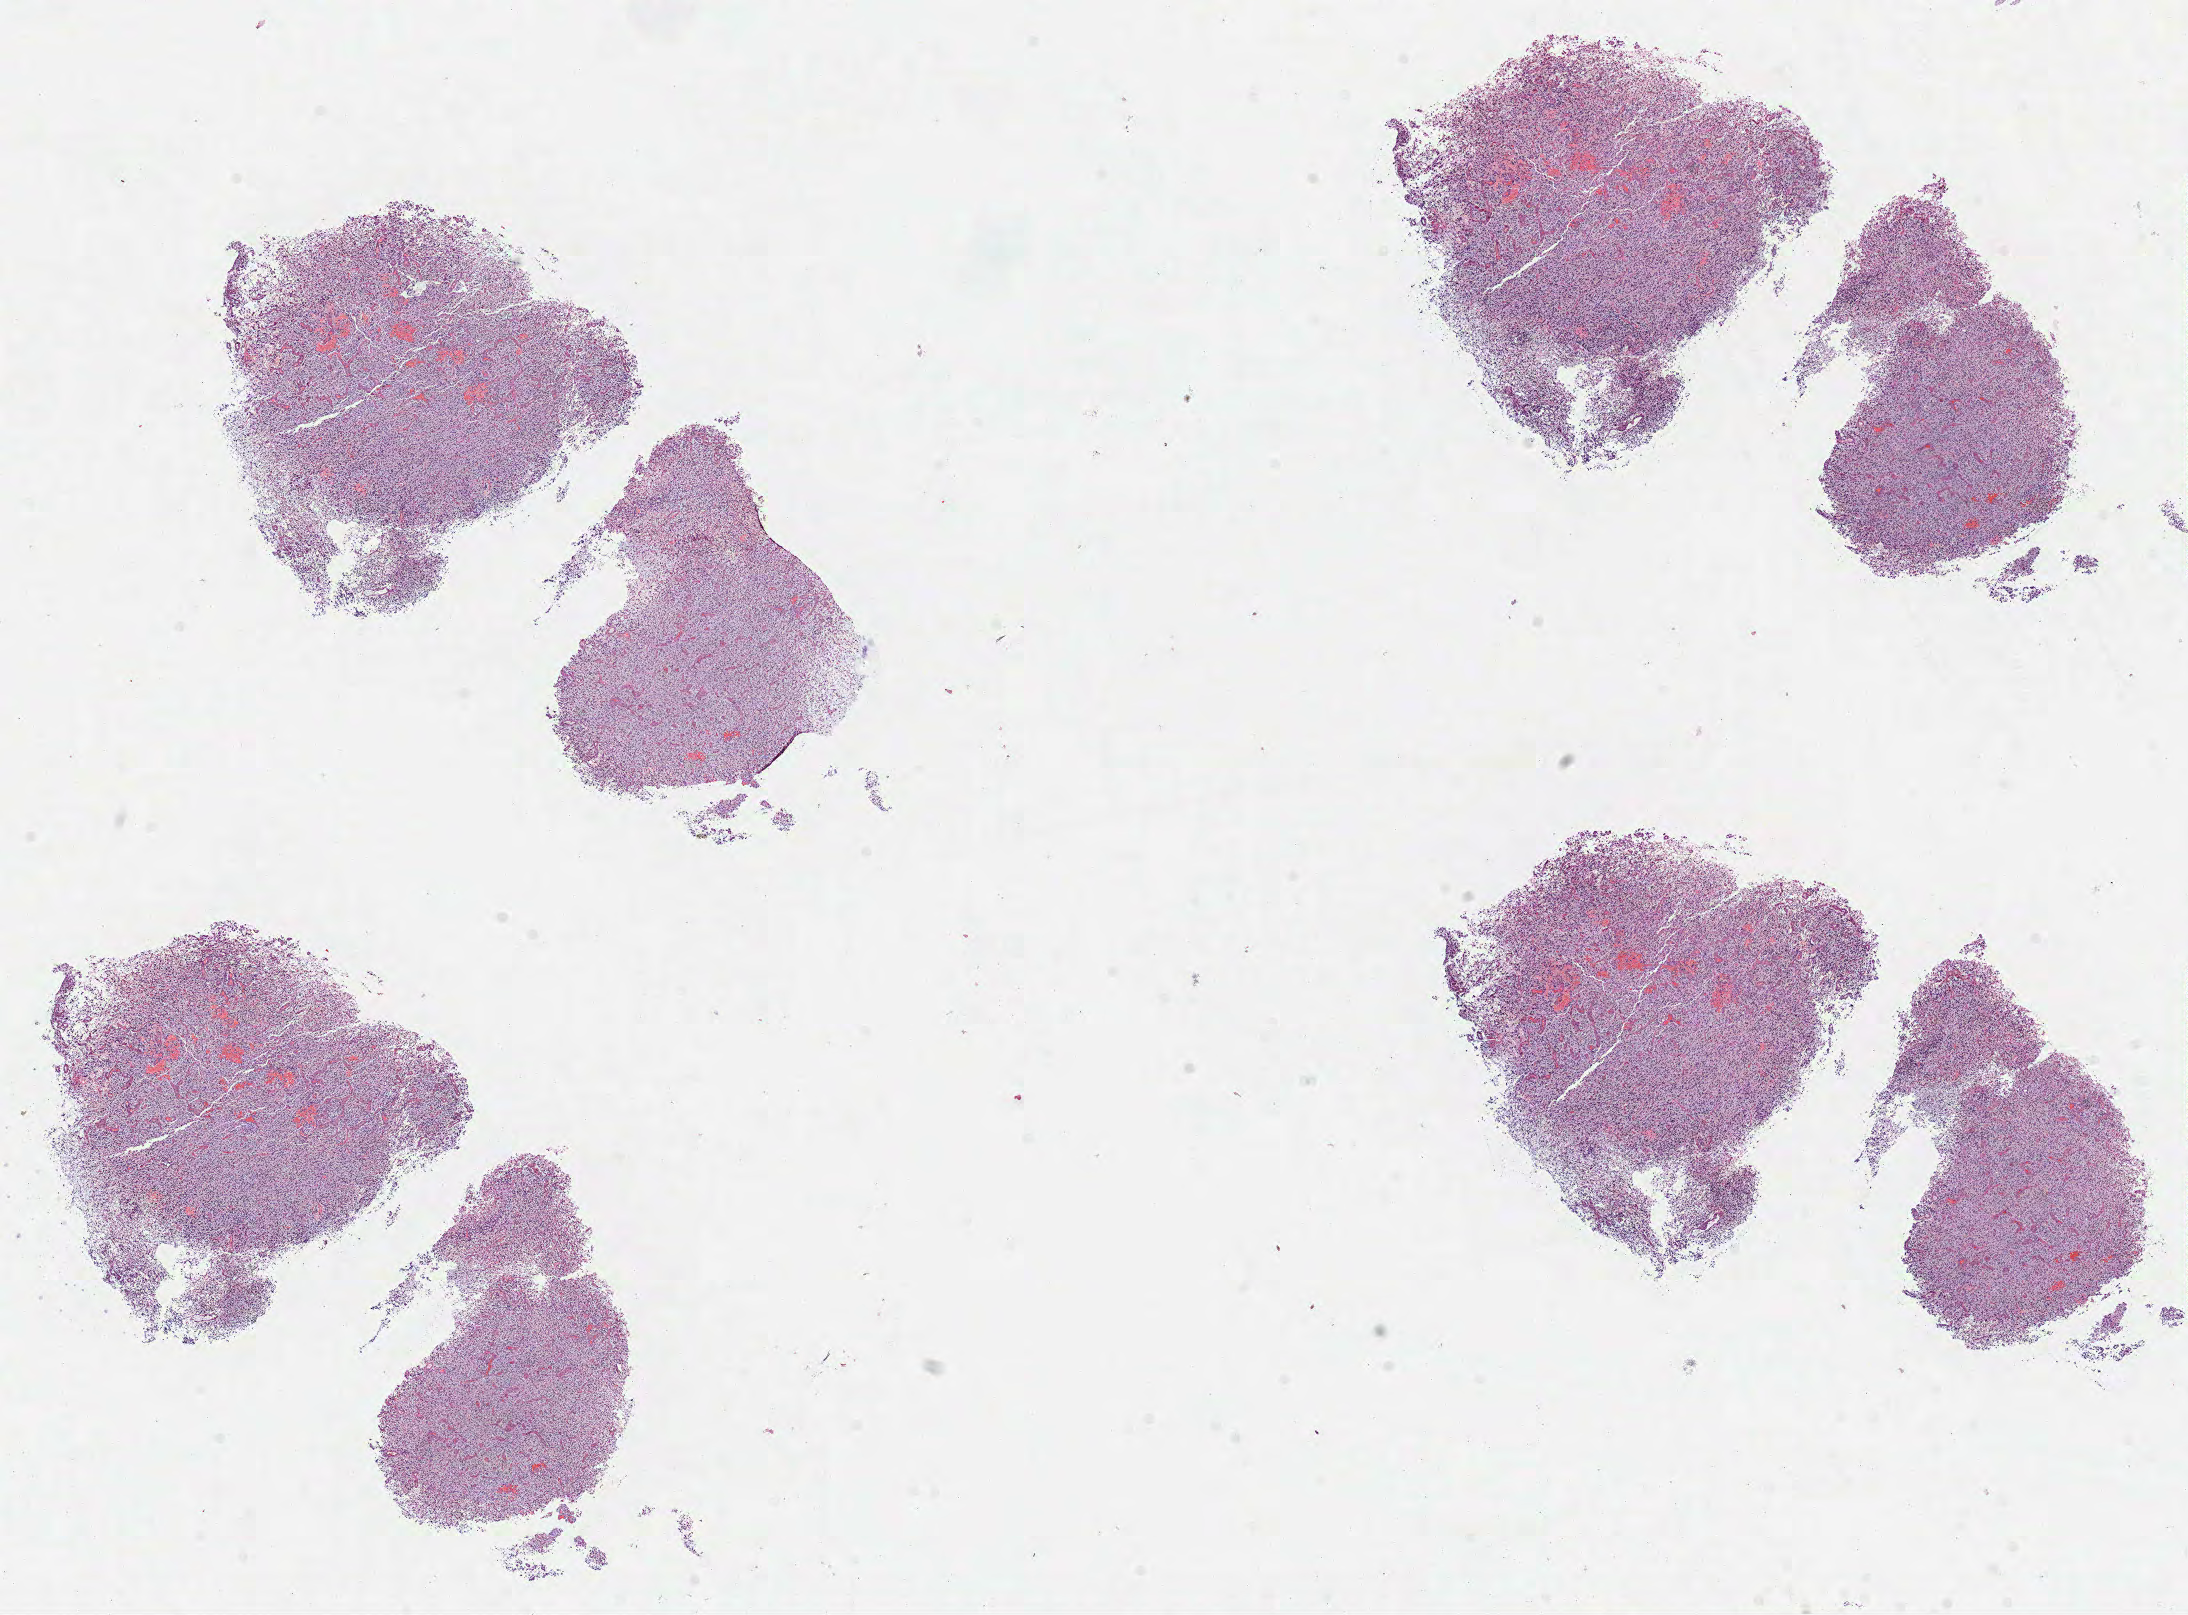
H&E-stained whole-slide image, low-resolution overview of the scanned area, about 17.6 x 13.0 mm (slide scanned at 40x). Formalin-fixed paraffin-embedded (FFPE) diagnostic section. Brain, primary tumour sample. Patient: female, age at initial diagnosis 44 years.
Diagnosis: Glioblastoma.